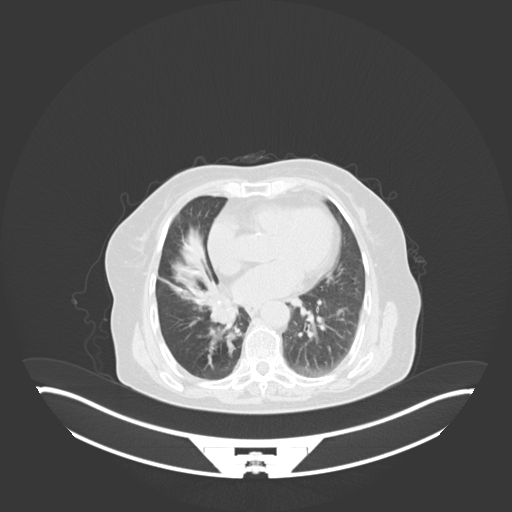
Chest CT, one axial slice; 120 kVp; lung window (W 1500 / L -600 HU); 512 × 512 image matrix. Female patient, age 75 years. Case-level facts recorded for this patient, not image findings: clinical TNM (as recorded): T1b N0 M1a.
Outlined on this slice (rectangle marked by the reading radiologist):
- lung tumour (recorded histology: squamous cell carcinoma): bounding box (x1, y1, x2, y2) in pixels: (208, 295, 241, 329)